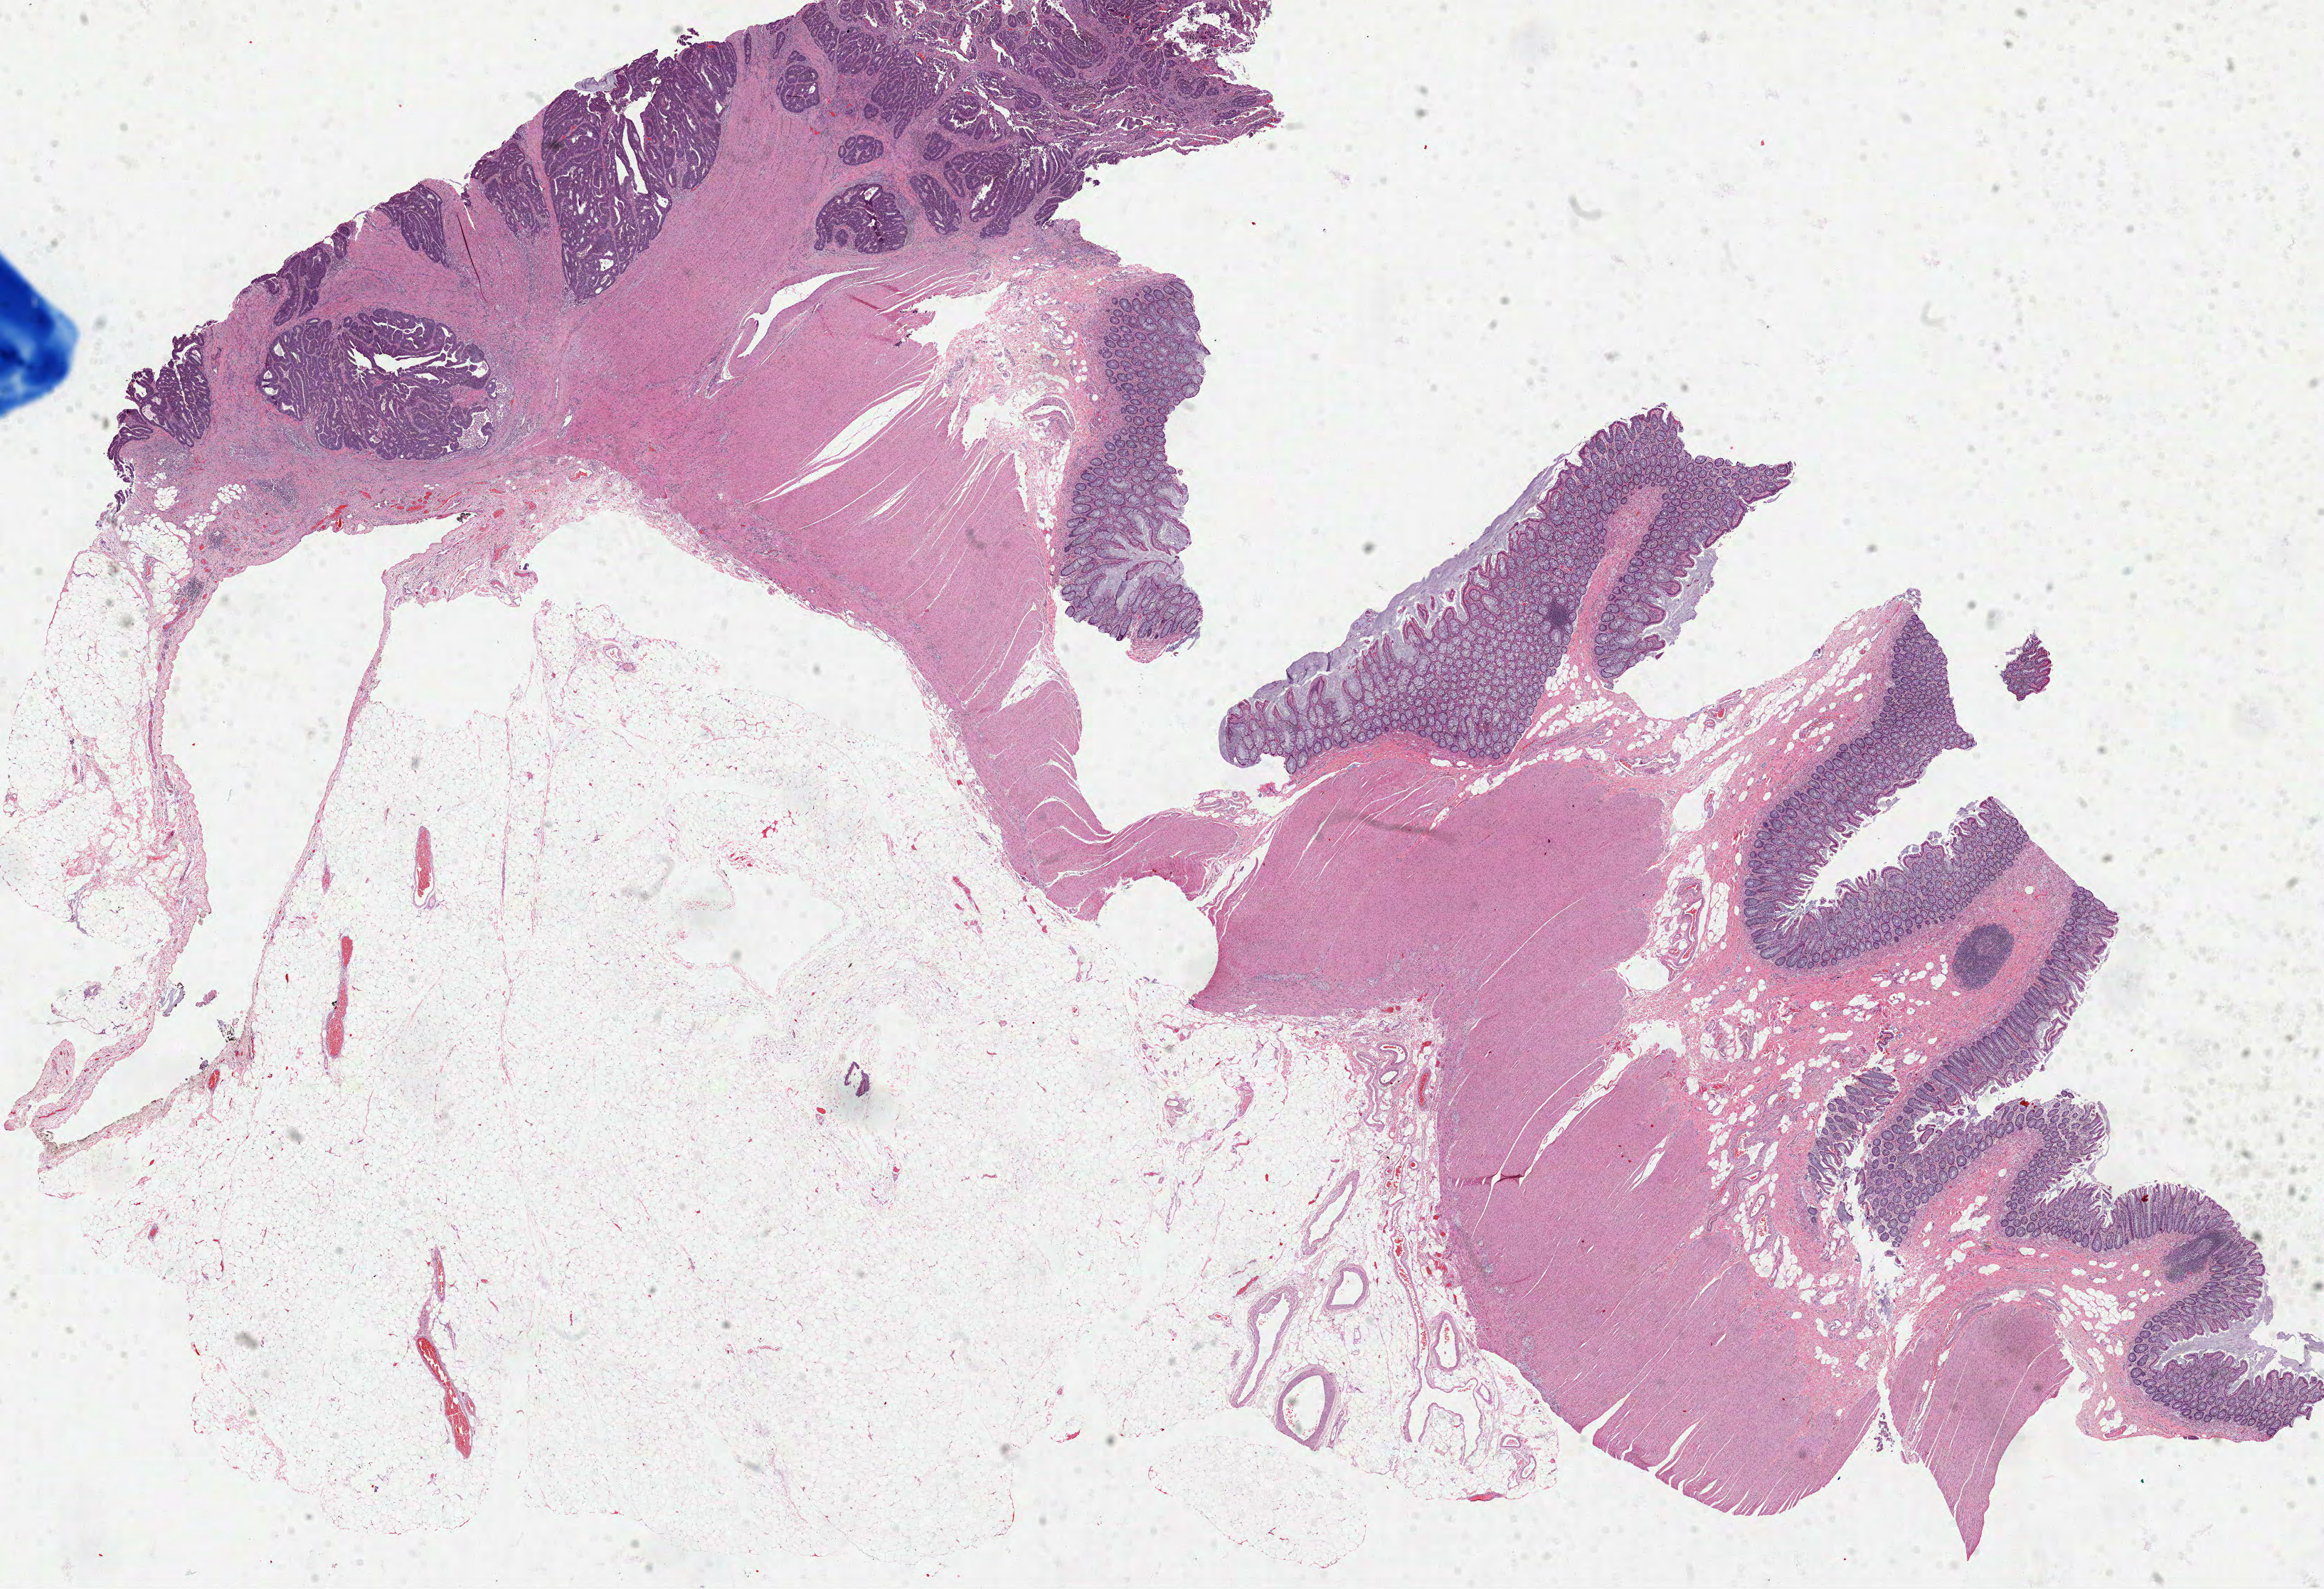
Whole-slide histology image, H&E-stained, low-resolution overview of the scanned area, about 26.3 x 18.0 mm; formalin-fixed paraffin-embedded (FFPE) diagnostic section; sample: primary tumour, rectum. Patient: female, age at initial diagnosis 49 years.
Lymph nodes positive (case pathology): 1 of 22 examined. TNM: T3 N1a M0. AJCC pathologic stage: IIIB (7th edition). Diagnosis: Adenocarcinoma, NOS.